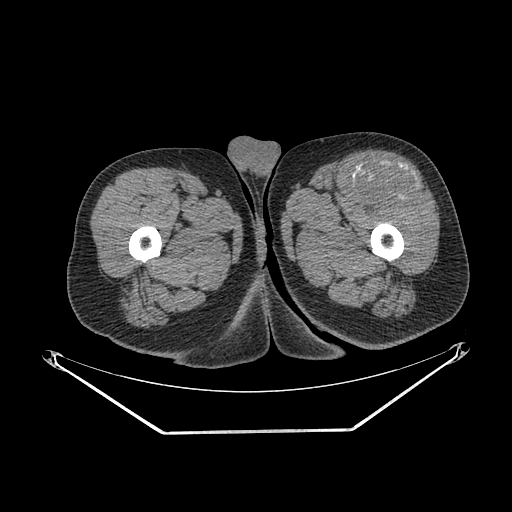
CT of an extremity soft-tissue mass (from a PET/CT study), one axial slice. Slice 251 of 267 in the series (ordered by position). Reconstruction kernel SOFT. 140 kVp. Soft-tissue window (W 400 / L 40 HU). 3.75 mm slice thickness. 512 × 512 image matrix, field of view 500 × 500 mm. Male patient. From the clinical record (not read from this slice): histological type: extraskeletal osteosarcoma; grade: high; site of the primary tumour: thigh.
Structures marked on this image (expert contour drawn on MRI and transferred to this co-registered scan by the dataset authors):
- gross tumour volume (mass): bounding box (x1, y1, x2, y2) in pixels: (358, 169, 423, 204)